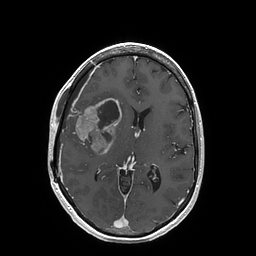
Brain MRI from a brain-tumour surgery series, one axial slice; position 82 of 202 along the scan axis; T1-weighted post-contrast; 256 × 256 image matrix, field of view 250 × 250 mm. From the clinical record (not read from this slice): histopathology: Glioblastoma; WHO grade: 4; IDH mutation: no; tumour location: Right Insular.
Structures marked on this image (outlined manually by an expert reader):
- tumour: bounding box <69,98,122,155> (left, top, right, bottom; pixels)